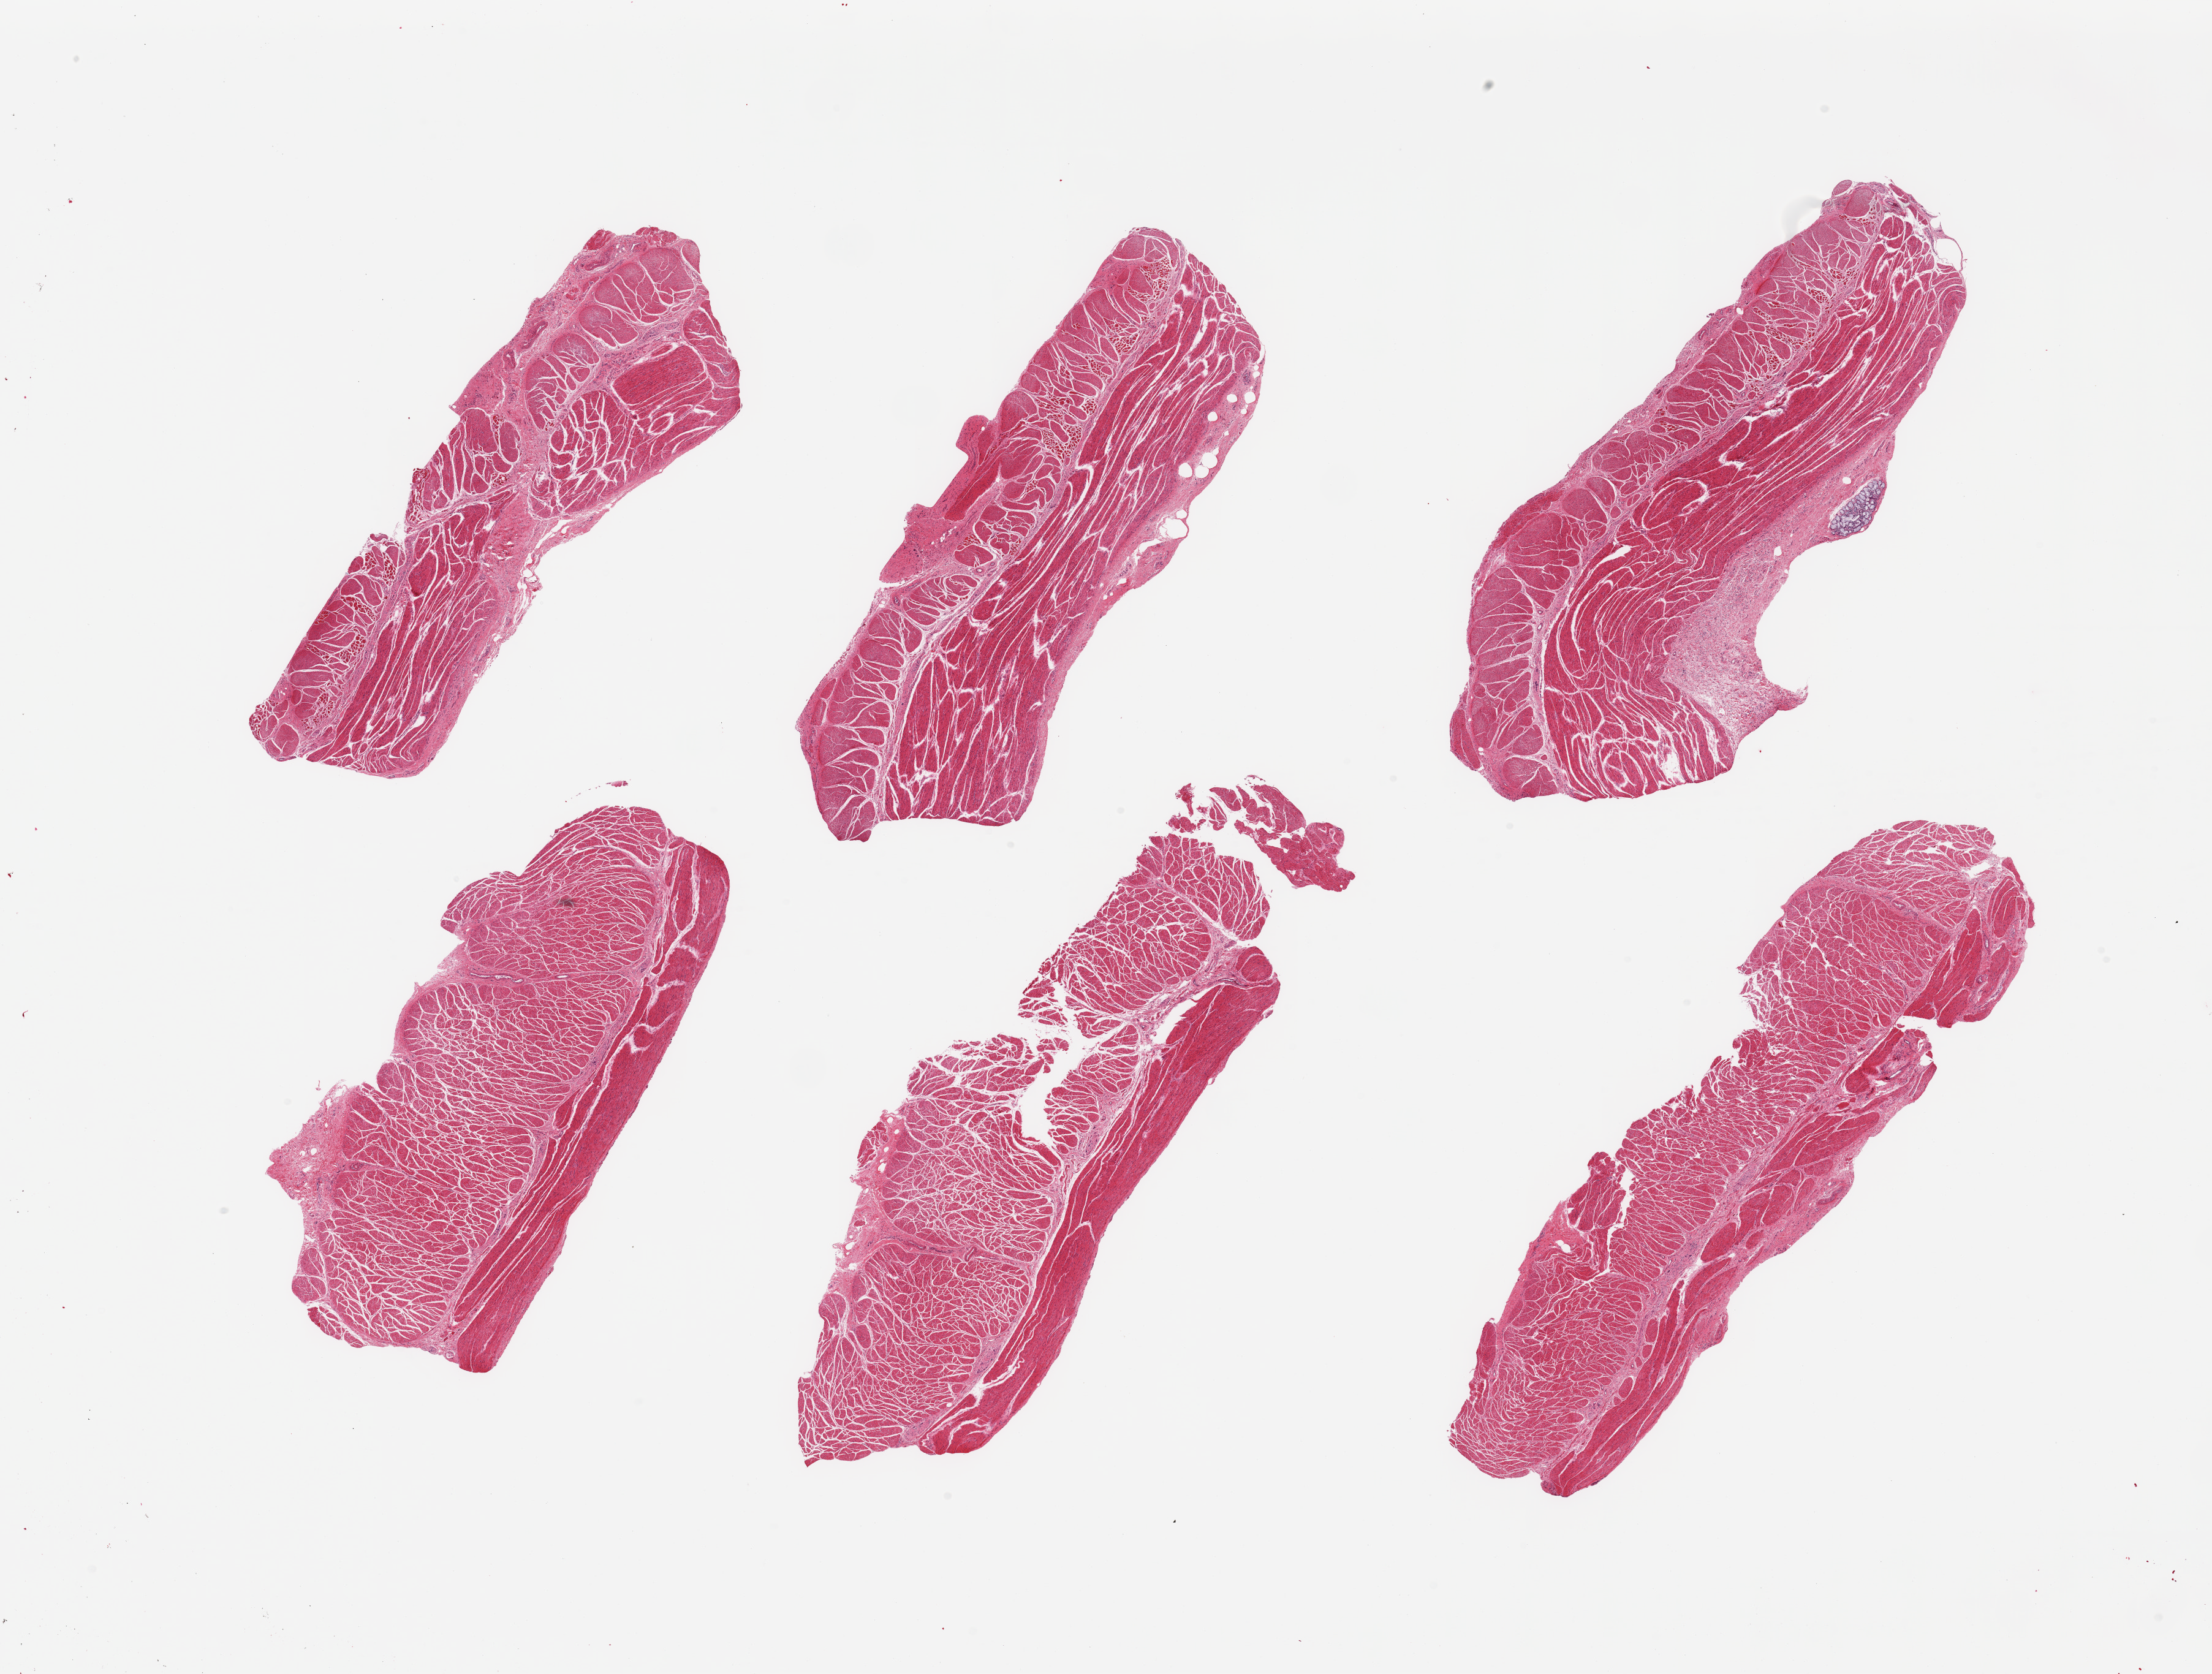
Digitized H&E-stained section, whole scanned area (about 28.5 x 21.6 mm, slide scanned at 20x) shown as a low-resolution overview; PAXgene-fixed paraffin-embedded (PFPE) section; target tissue: esophageal muscle; tissue donor sample. Donor: male.
- pathologist's review note for this sample: 6 pieces; well trimmed, but 3 of 6 include admixture of smooth and skeletal muscle suggesting sampling of upper esophagus